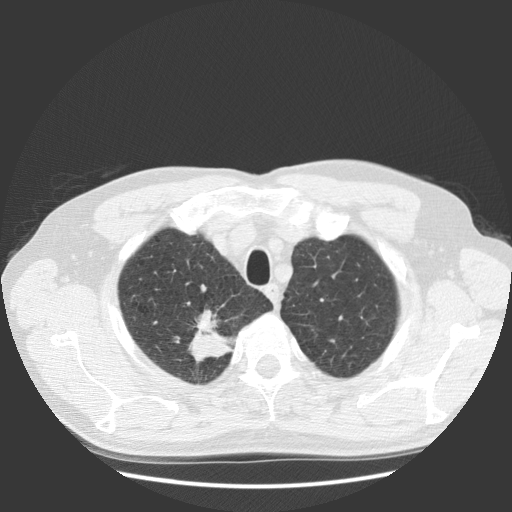
Axial slice from a low-dose chest CT screening exam; first (baseline) screen; lung window (W 1500 / L -600 HU); 2.5 mm slice thickness; standard (soft-tissue) reconstruction kernel (STANDARD); slice 109 of 131 in the series. Male participant, aged 63 years at enrolment.
• Expert-annotated lung lesion, bounding box (x1, y1, x2, y2) in pixels: (168, 321, 239, 384).
• The screening reader recorded 2 non-calcified nodules or masses ≥4 mm on this exam (right upper lobe, right upper lobe); which of them this box marks is not recorded.
• Later outcome: lung cancer diagnosed 30 days after this screen — squamous cell carcinoma, NOS, right upper lobe, stage IIIB (AJCC 6th edition), 35 mm at pathology.